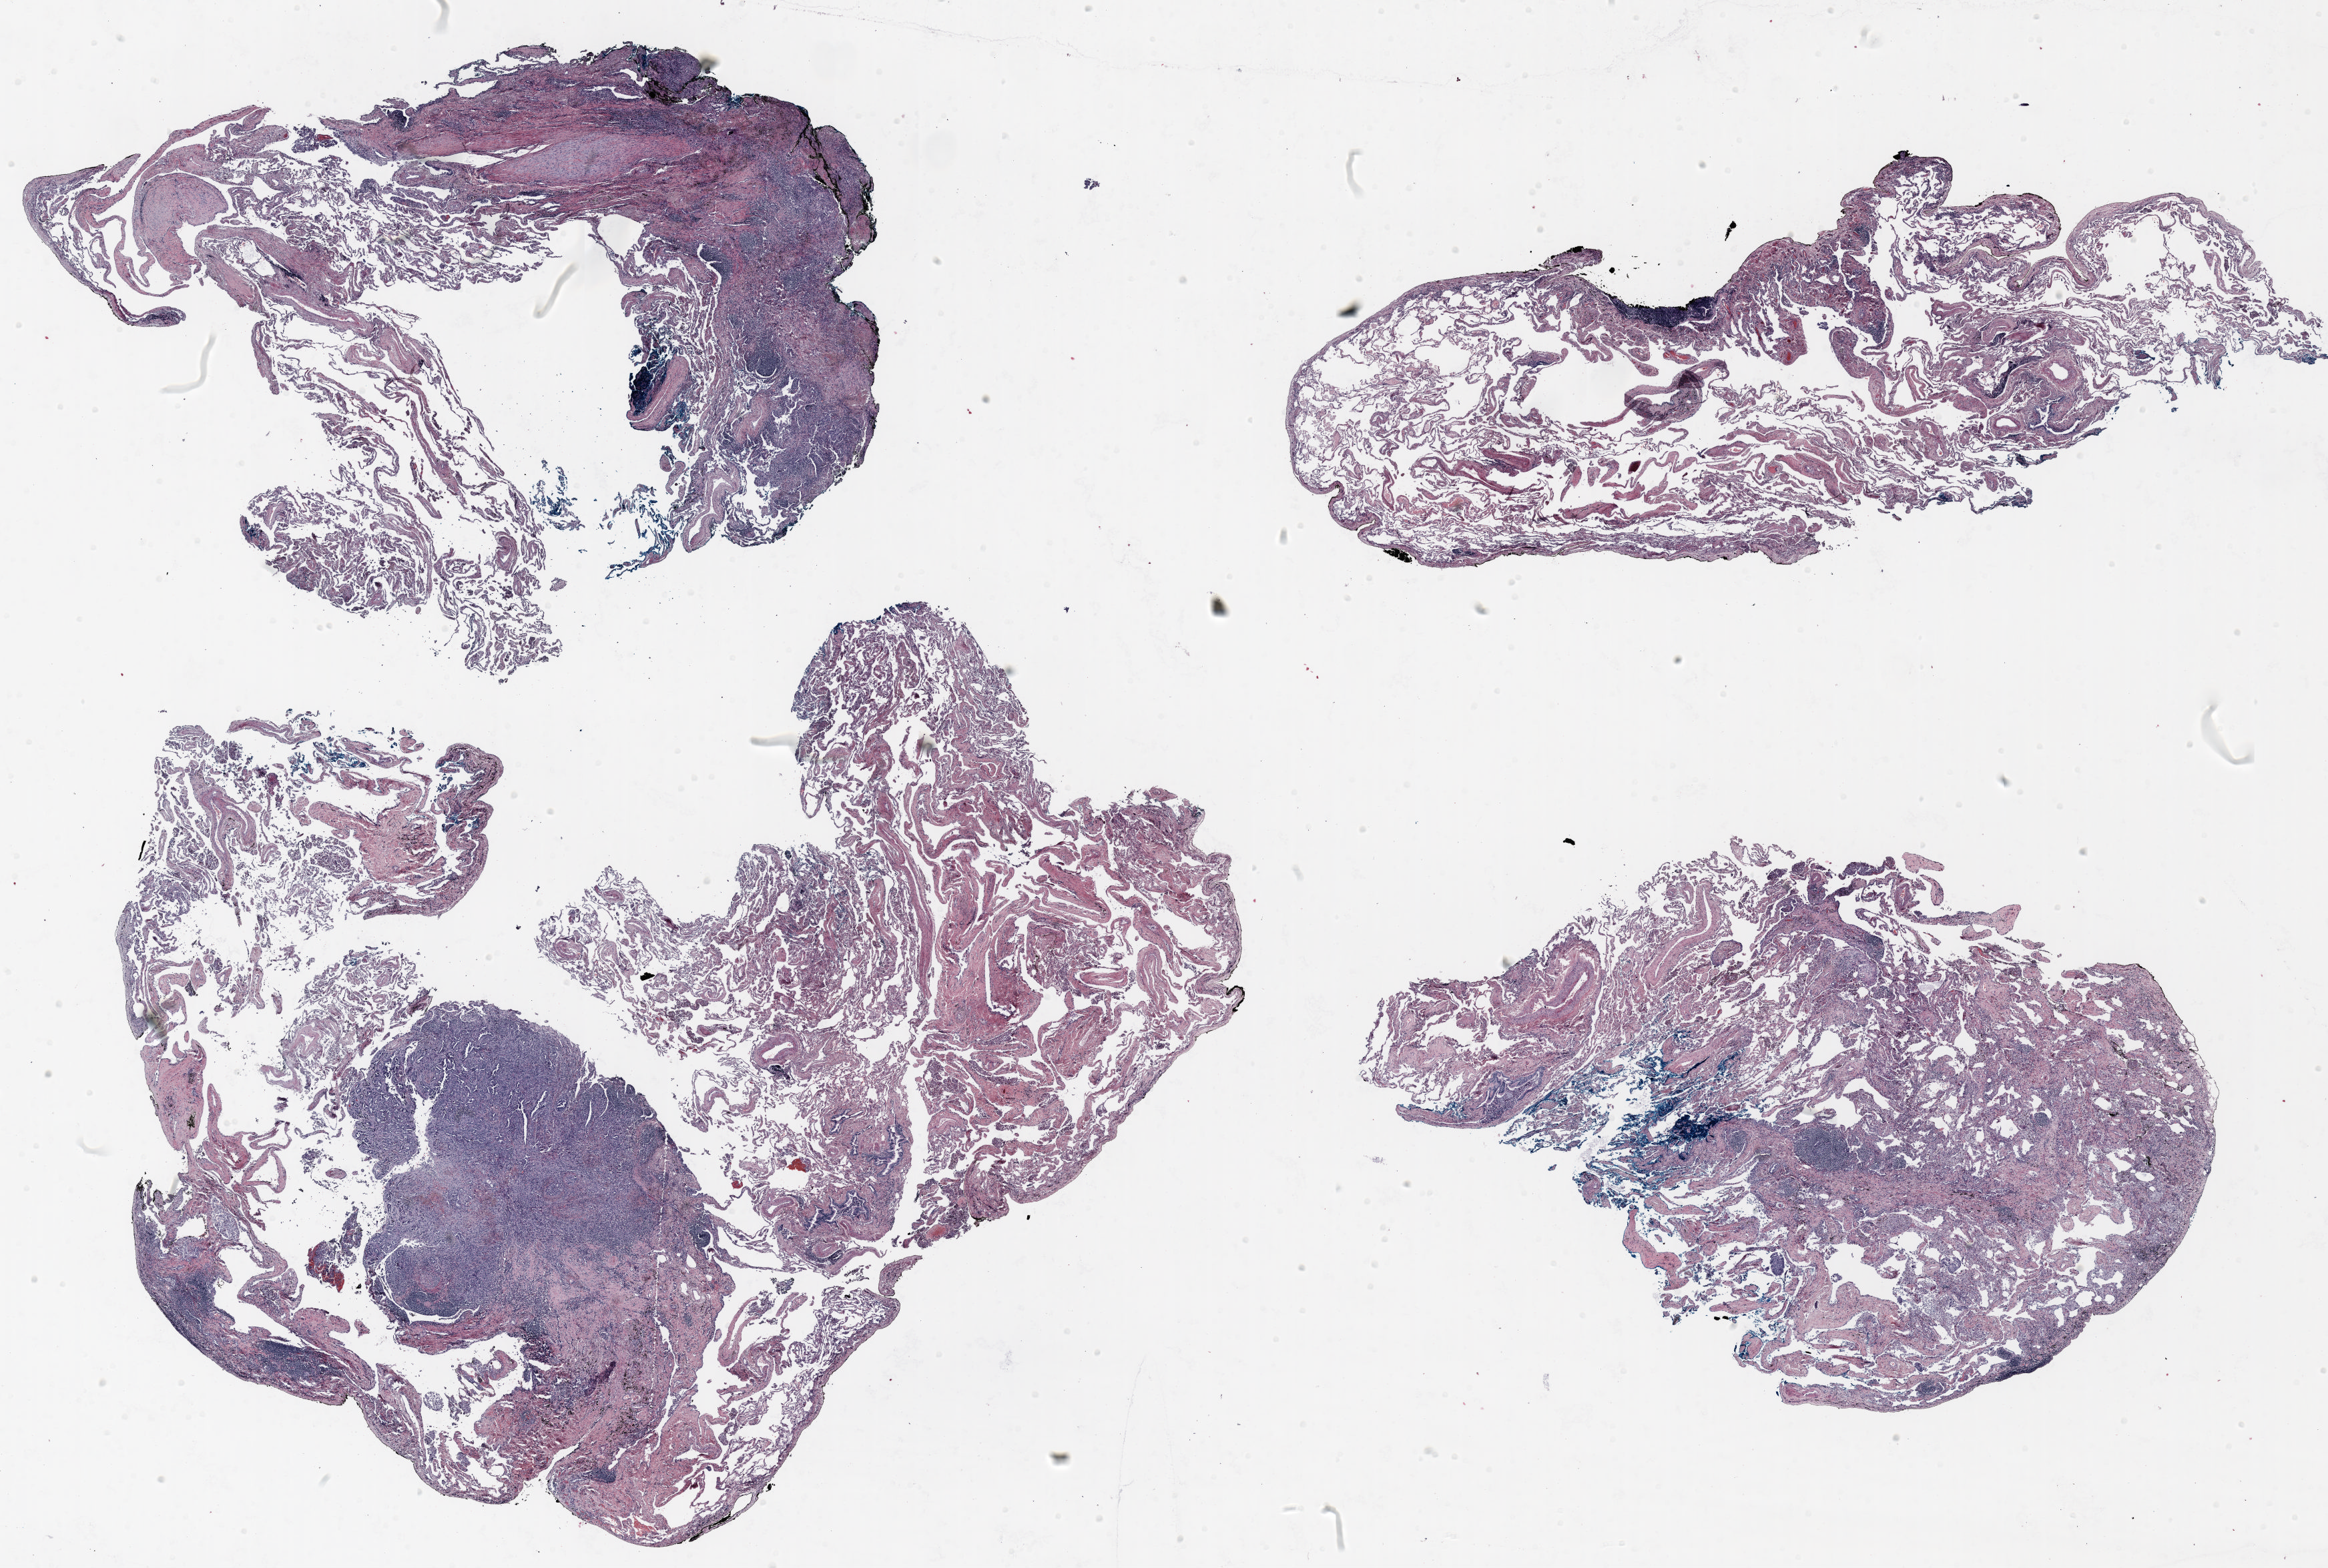
Hematoxylin and eosin (H&E) stained whole-slide image — low-resolution overview of the scanned area, about 28.0 x 18.9 mm; FFPE section; lung. Female patient, aged 66 at enrolment. Current smoker at enrolment. Grade: moderately differentiated (G2).
Stage (AJCC 6th edition): IB. Tumour size (pathology): 17 mm. Participant's lung-cancer diagnosis: Adenocarcinoma, NOS (ICD-O-3 8140/3). Primary tumour location (clinical record): left upper lobe. Note: participant had 2 primary lung cancers recorded; fields above describe the first.